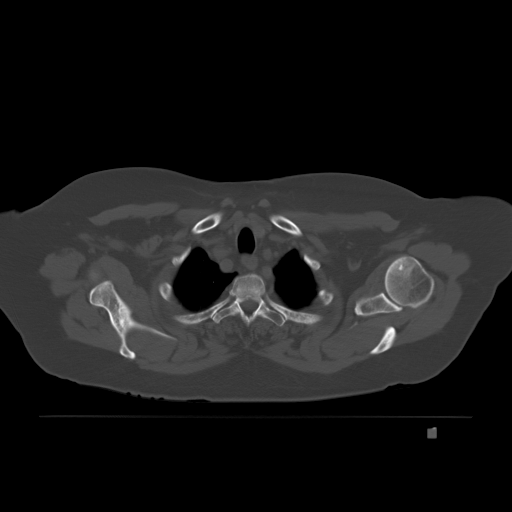
CT including the spine, one axial slice. Position 169 of 221 along the scan axis. Bone window (W 1800 / L 400 HU). 512 × 512 image matrix, field of view 474 × 474 mm. Patient: female, 63 years. Case-level facts recorded for this patient, not image findings: primary cancer: breast.
Annotated regions visible in this slice (semi-automatically segmented with operator editing):
- T3 vertebra: bounding box [x1, y1, x2, y2] px = [262, 315, 284, 320]